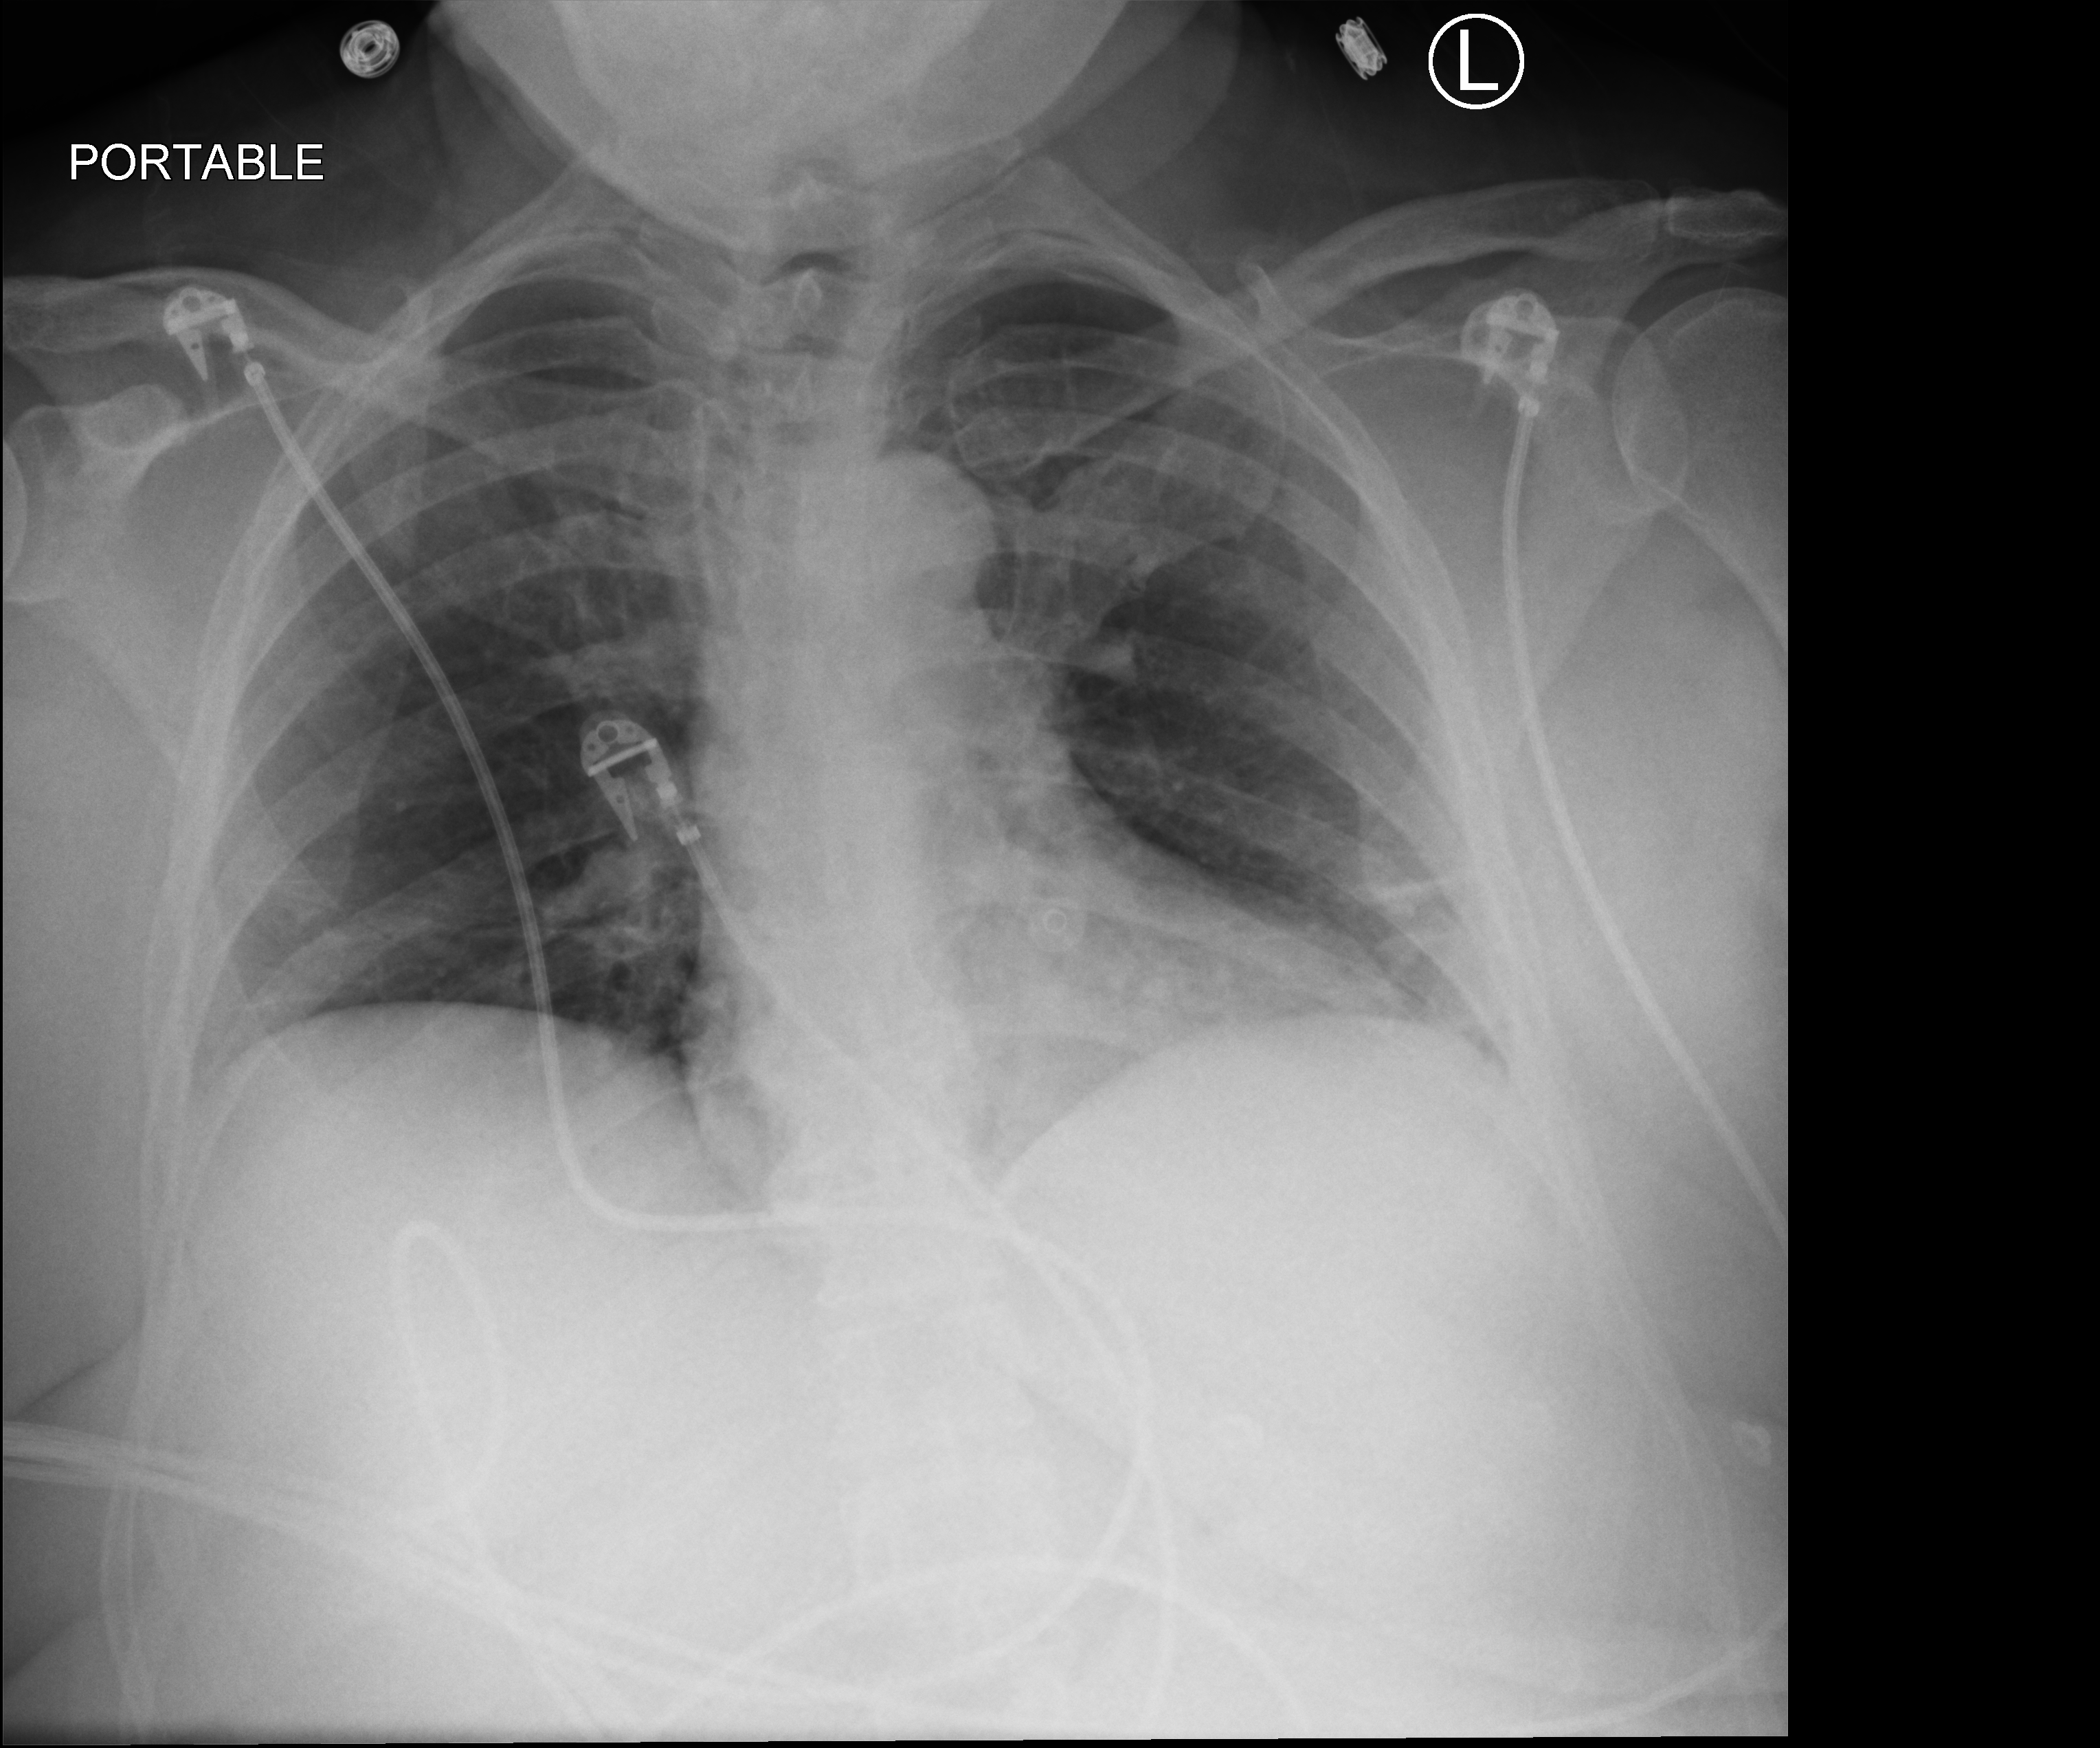
Portable chest radiograph; anteroposterior (AP) projection. Patient hospitalised with COVID-19; female, aged 60–74 years.
From the hospital-stay record, not from the radiograph (when in the stay this image was taken is not recorded): admitted to intensive care during this hospital stay: yes.